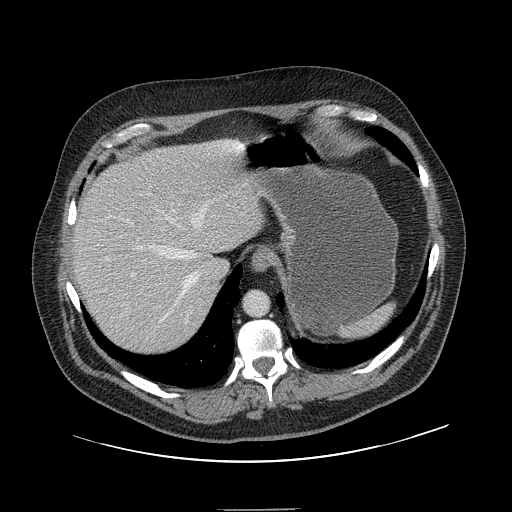
Contrast-enhanced abdominal CT, one axial slice. Position 118 of 154 along the scan axis. Intravenous contrast given. Soft-tissue window (W 400 / L 40 HU). 2.5 mm slice thickness. 512 × 512 image matrix, field of view 451 × 451 mm. Male patient, age 61 years. Case-level facts recorded for this patient, not image findings: diagnosis: colorectal cancer liver metastases, imaged before liver resection; multiple liver metastases: yes; largest metastasis: 2.6 cm; disease in both lobes: yes.
Annotated regions visible in this slice (outlined manually by an expert reader):
- hepatic veins: box from (x=137, y=193) to (x=214, y=320) px
- liver: (x=72, y=141)–(x=265, y=355)
- planned liver remnant (the part of the liver to remain after resection): (x=72, y=143)–(x=265, y=352)
- portal vein (with intrahepatic branches): (x=119, y=217)–(x=162, y=308)